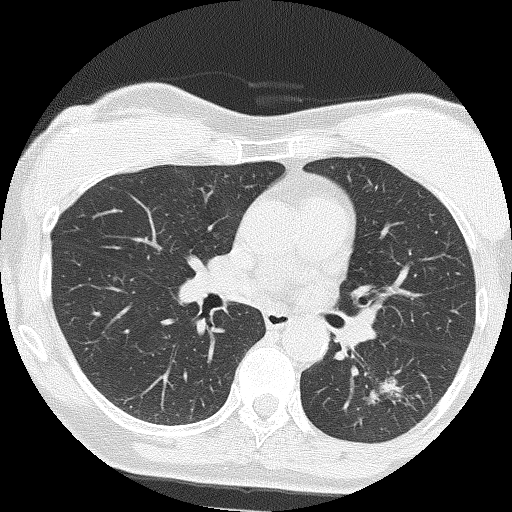
Axial slice from a low-dose chest CT screening exam; second screening round (one year after baseline); lung window (W 1500 / L -600 HU); slice 71 of 159 in the series; 512 × 512 image matrix. Female, age 64 years at enrolment. Former smoker at enrolment.
Expert reader's lesion annotation, box from (x=359, y=363) to (x=445, y=438) px. The screening reader recorded 3 non-calcified nodules or masses ≥4 mm on this exam (right upper lobe, right upper lobe, right middle lobe); which of them this box marks is not recorded. Official screen result: positive, other. Participant outcome: lung cancer diagnosed 576 days after this screen — adenocarcinoma, NOS, left lower lobe, moderately differentiated (G2), stage IA (AJCC 6th edition), 17 mm at pathology.